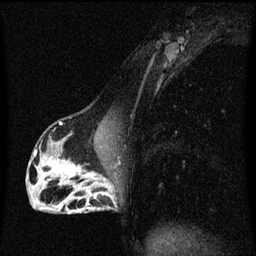
Breast MRI (dynamic contrast-enhanced), one sagittal slice. Position 29 of 60 along the scan axis. Dynamic contrast-enhanced series, image 2 of 3 at this slice position (ordered by acquisition). 1.5 T. TE 4.2 ms, TR 8.4 ms. 256 × 256 image matrix, field of view 200 × 200 mm. Female patient, age 40 years.
Structures marked on this image (semi-automatically segmented with operator editing):
- analysis volume of interest (the breast-tissue region the enhancement analysis was run in; not a lesion): box from (x=76, y=172) to (x=115, y=213) px
- tumour enhancement mask (voxels above the 70 % enhancement threshold inside the analysis volume of interest): (x=76, y=172)–(x=115, y=213)